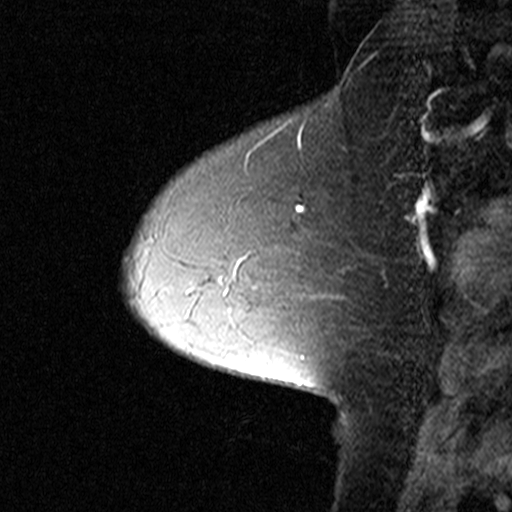
Breast MRI (dynamic contrast-enhanced), one sagittal slice; slice 12 of 44 in the series (ordered by position); dynamic contrast-enhanced study with each time point stored as its own series, time point 2 of 3 at this slice position (early post-contrast, ordered by acquisition time); 1.5 T; TE 4.5 ms, TR 11 ms; 3 mm slice thickness; 512 × 512 image matrix. Female patient, age 50 years. From the clinical record (not read from this slice): setting: breast cancer imaged before/during neoadjuvant chemotherapy; receptor status: HR-positive, HER2-negative.
Structures marked on this image (semi-automatic segmentation, software-assisted and operator-edited):
- analysis volume of interest (the breast-tissue region the enhancement analysis was run in; not a lesion): bounding box [x1, y1, x2, y2] px = [126, 162, 290, 291]
- tumour enhancement mask (voxels above the 90 % enhancement threshold inside the analysis volume of interest): [245, 164, 273, 172]